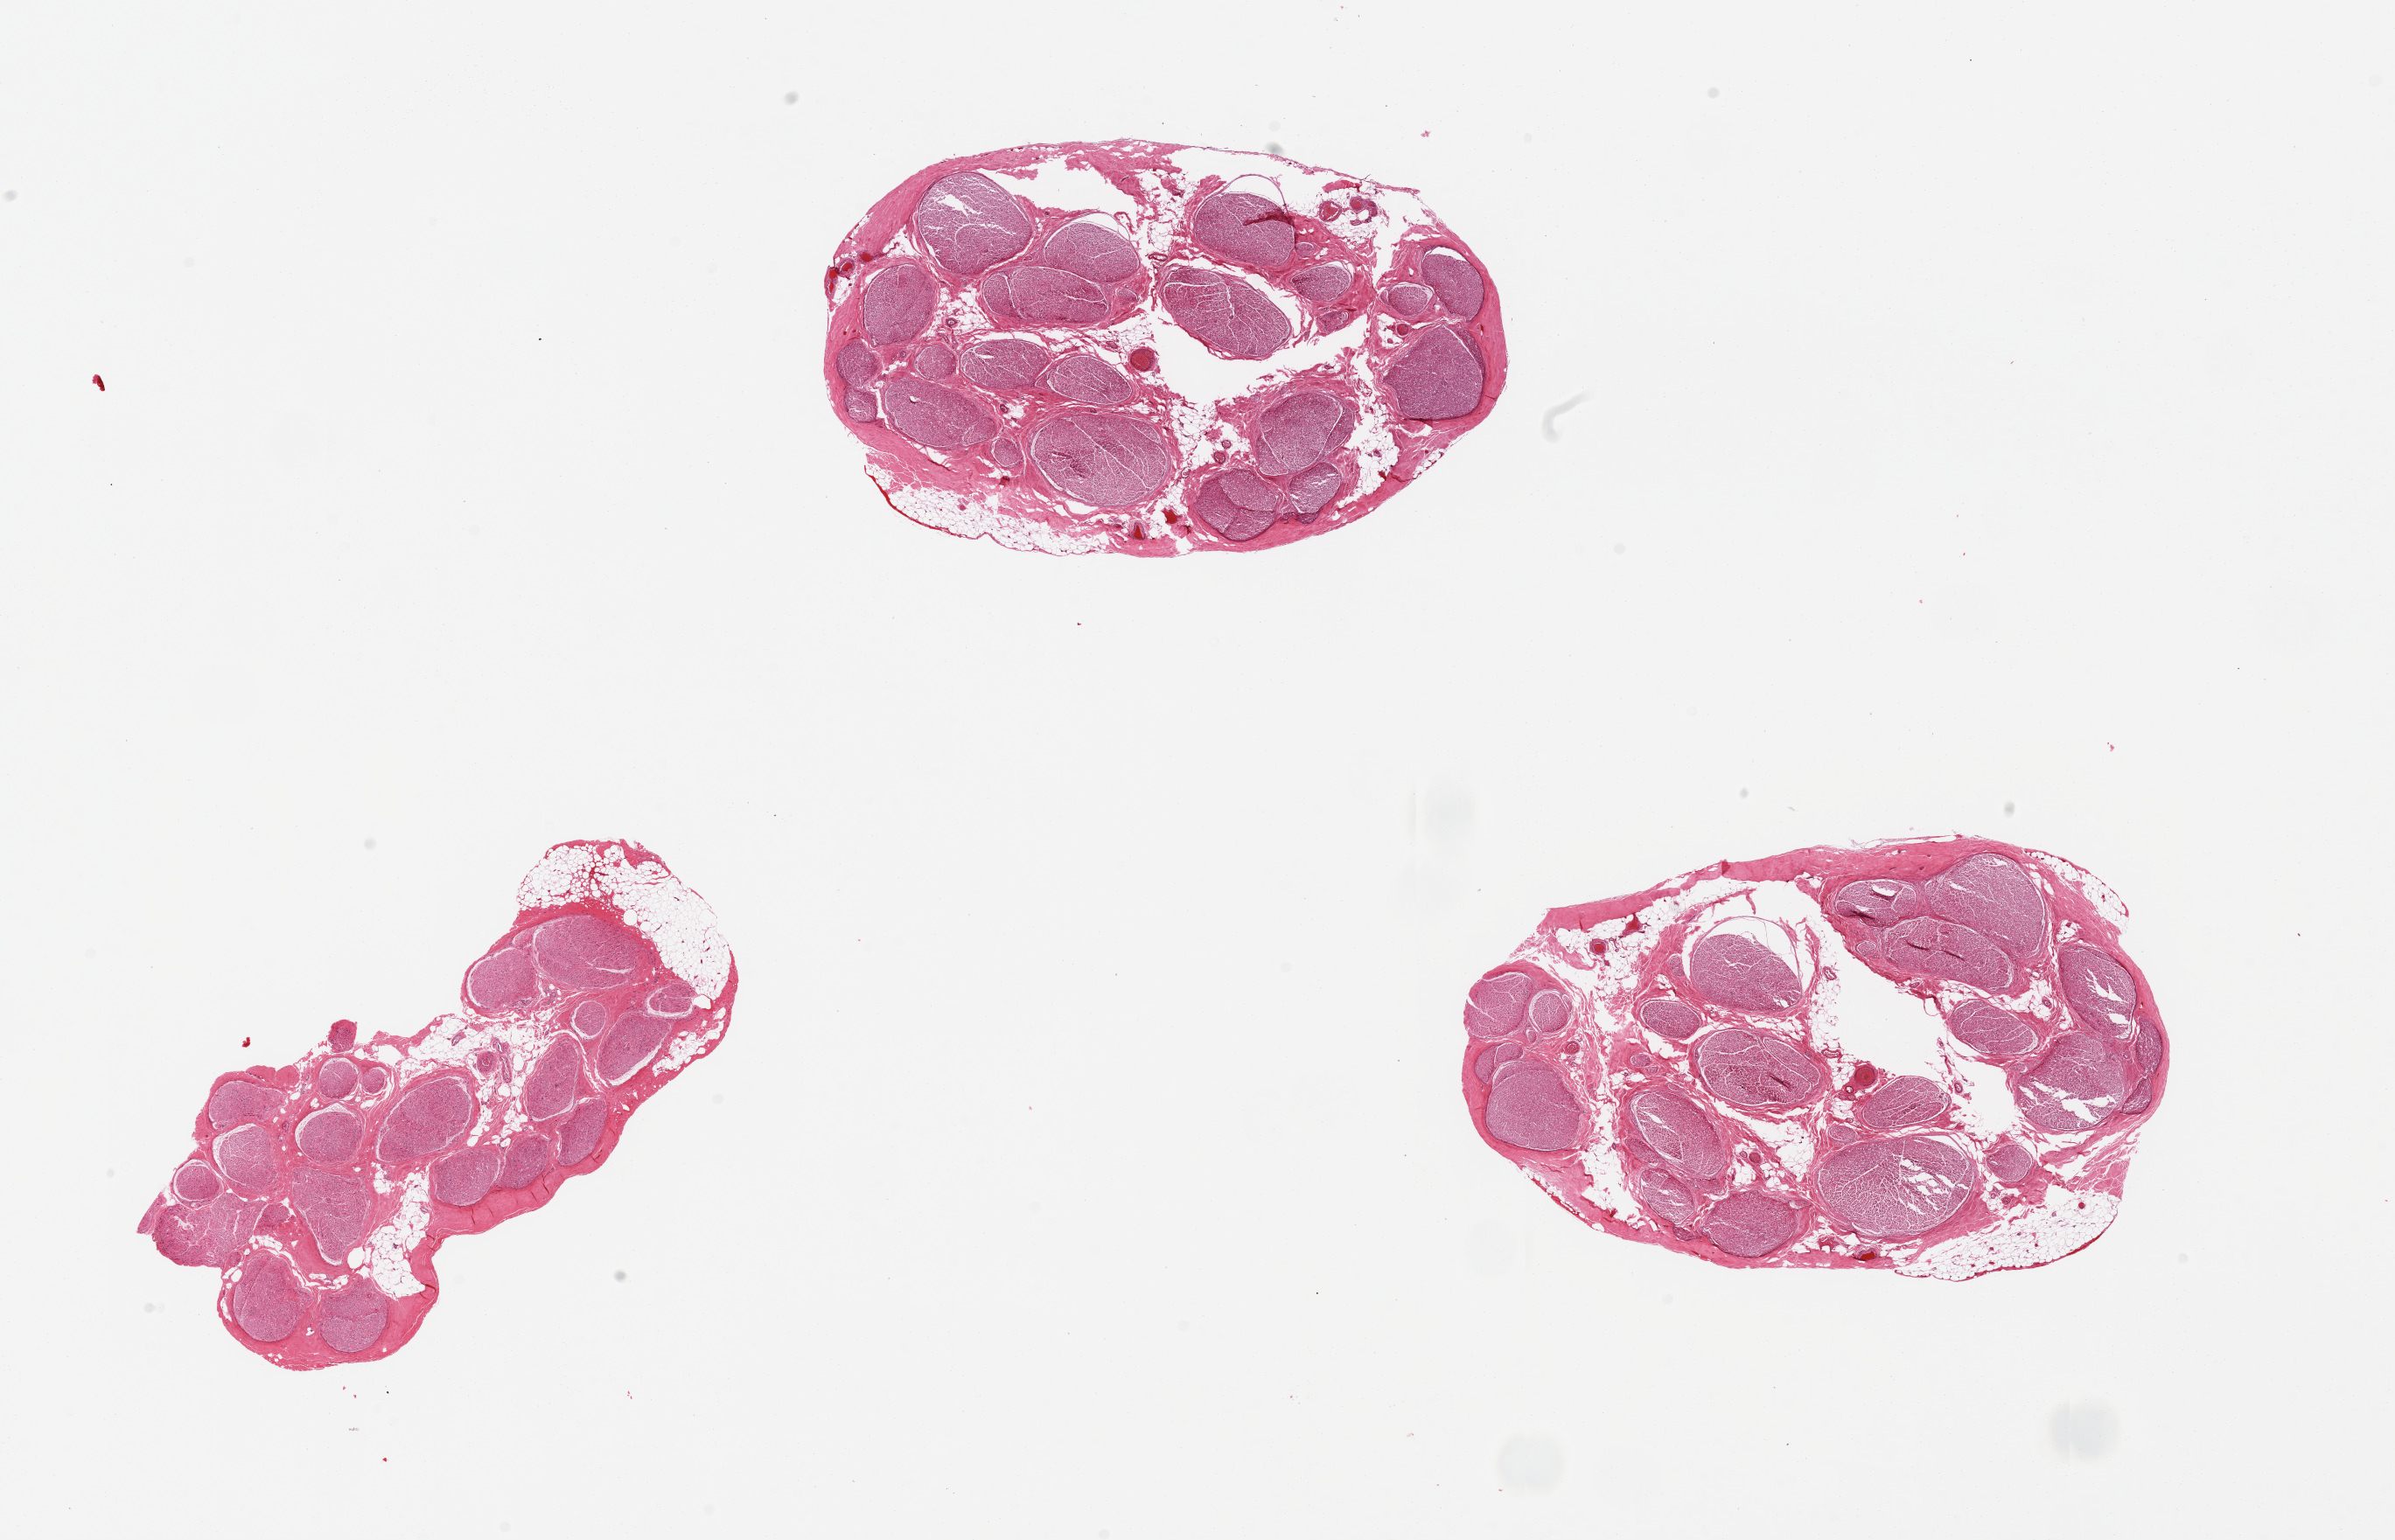
H&E whole-slide image, a low-resolution overview of the entire scanned area, about 21.7 x 13.9 mm. PAXgene-fixed, paraffin-embedded tissue. Section of tibial nerve (target tissue). Tissue donor sample. Donor: male.
• reviewer comment on this tissue sample: 3 pieces, minimal adherent fat, good specimens